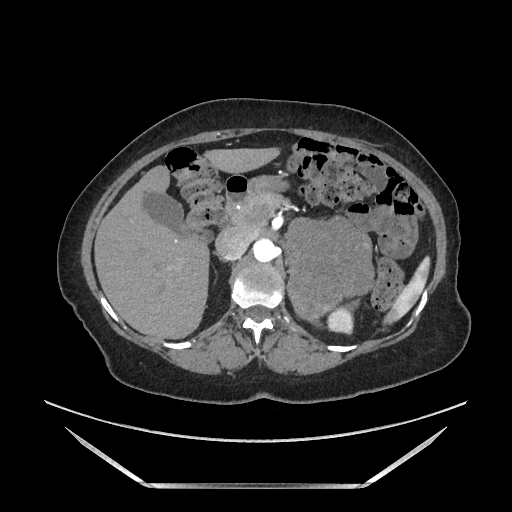
Contrast-enhanced abdominal CT, one axial slice; slice 105 of 205 in the series (ordered by position); soft-tissue window (W 400 / L 40 HU); 1.25 mm slice thickness; 512 × 512 image matrix, field of view 440 × 440 mm. Female patient. From the clinical record (not read from this slice): diagnosis: adrenocortical carcinoma; tumour side: left adrenal; tumour size at pathology: 12.5 cm; Ki-67 index: 39 %; stage (as recorded): 3.
Structures marked on this image (semi-automatic segmentation, software-assisted and operator-edited):
- mass: bounding box <288,219,373,317> (left, top, right, bottom; pixels)